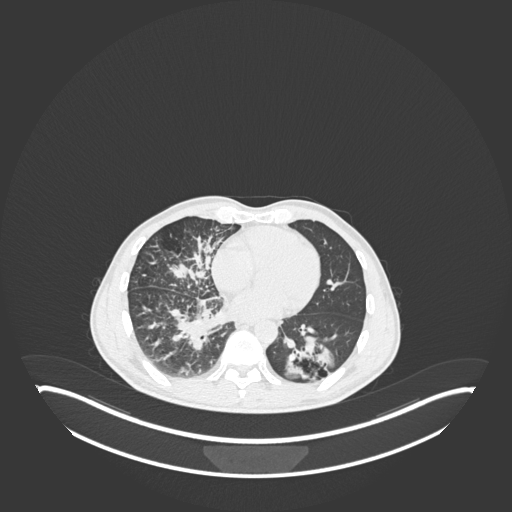
Chest CT, one axial slice; slice 94 of 237 in the series (ordered by position); lung window (W 1500 / L -600 HU); 1 mm slice thickness; 512 × 512 image matrix, field of view 500 × 500 mm. Male patient, age 49 years. Case-level facts recorded for this patient, not image findings: clinical TNM (as recorded): T2b N1 M0.
Annotated regions visible in this slice (bounding box drawn by a radiologist):
- lung tumour (recorded histology: adenocarcinoma): bounding box (x1, y1, x2, y2) in pixels: (282, 329, 339, 381)